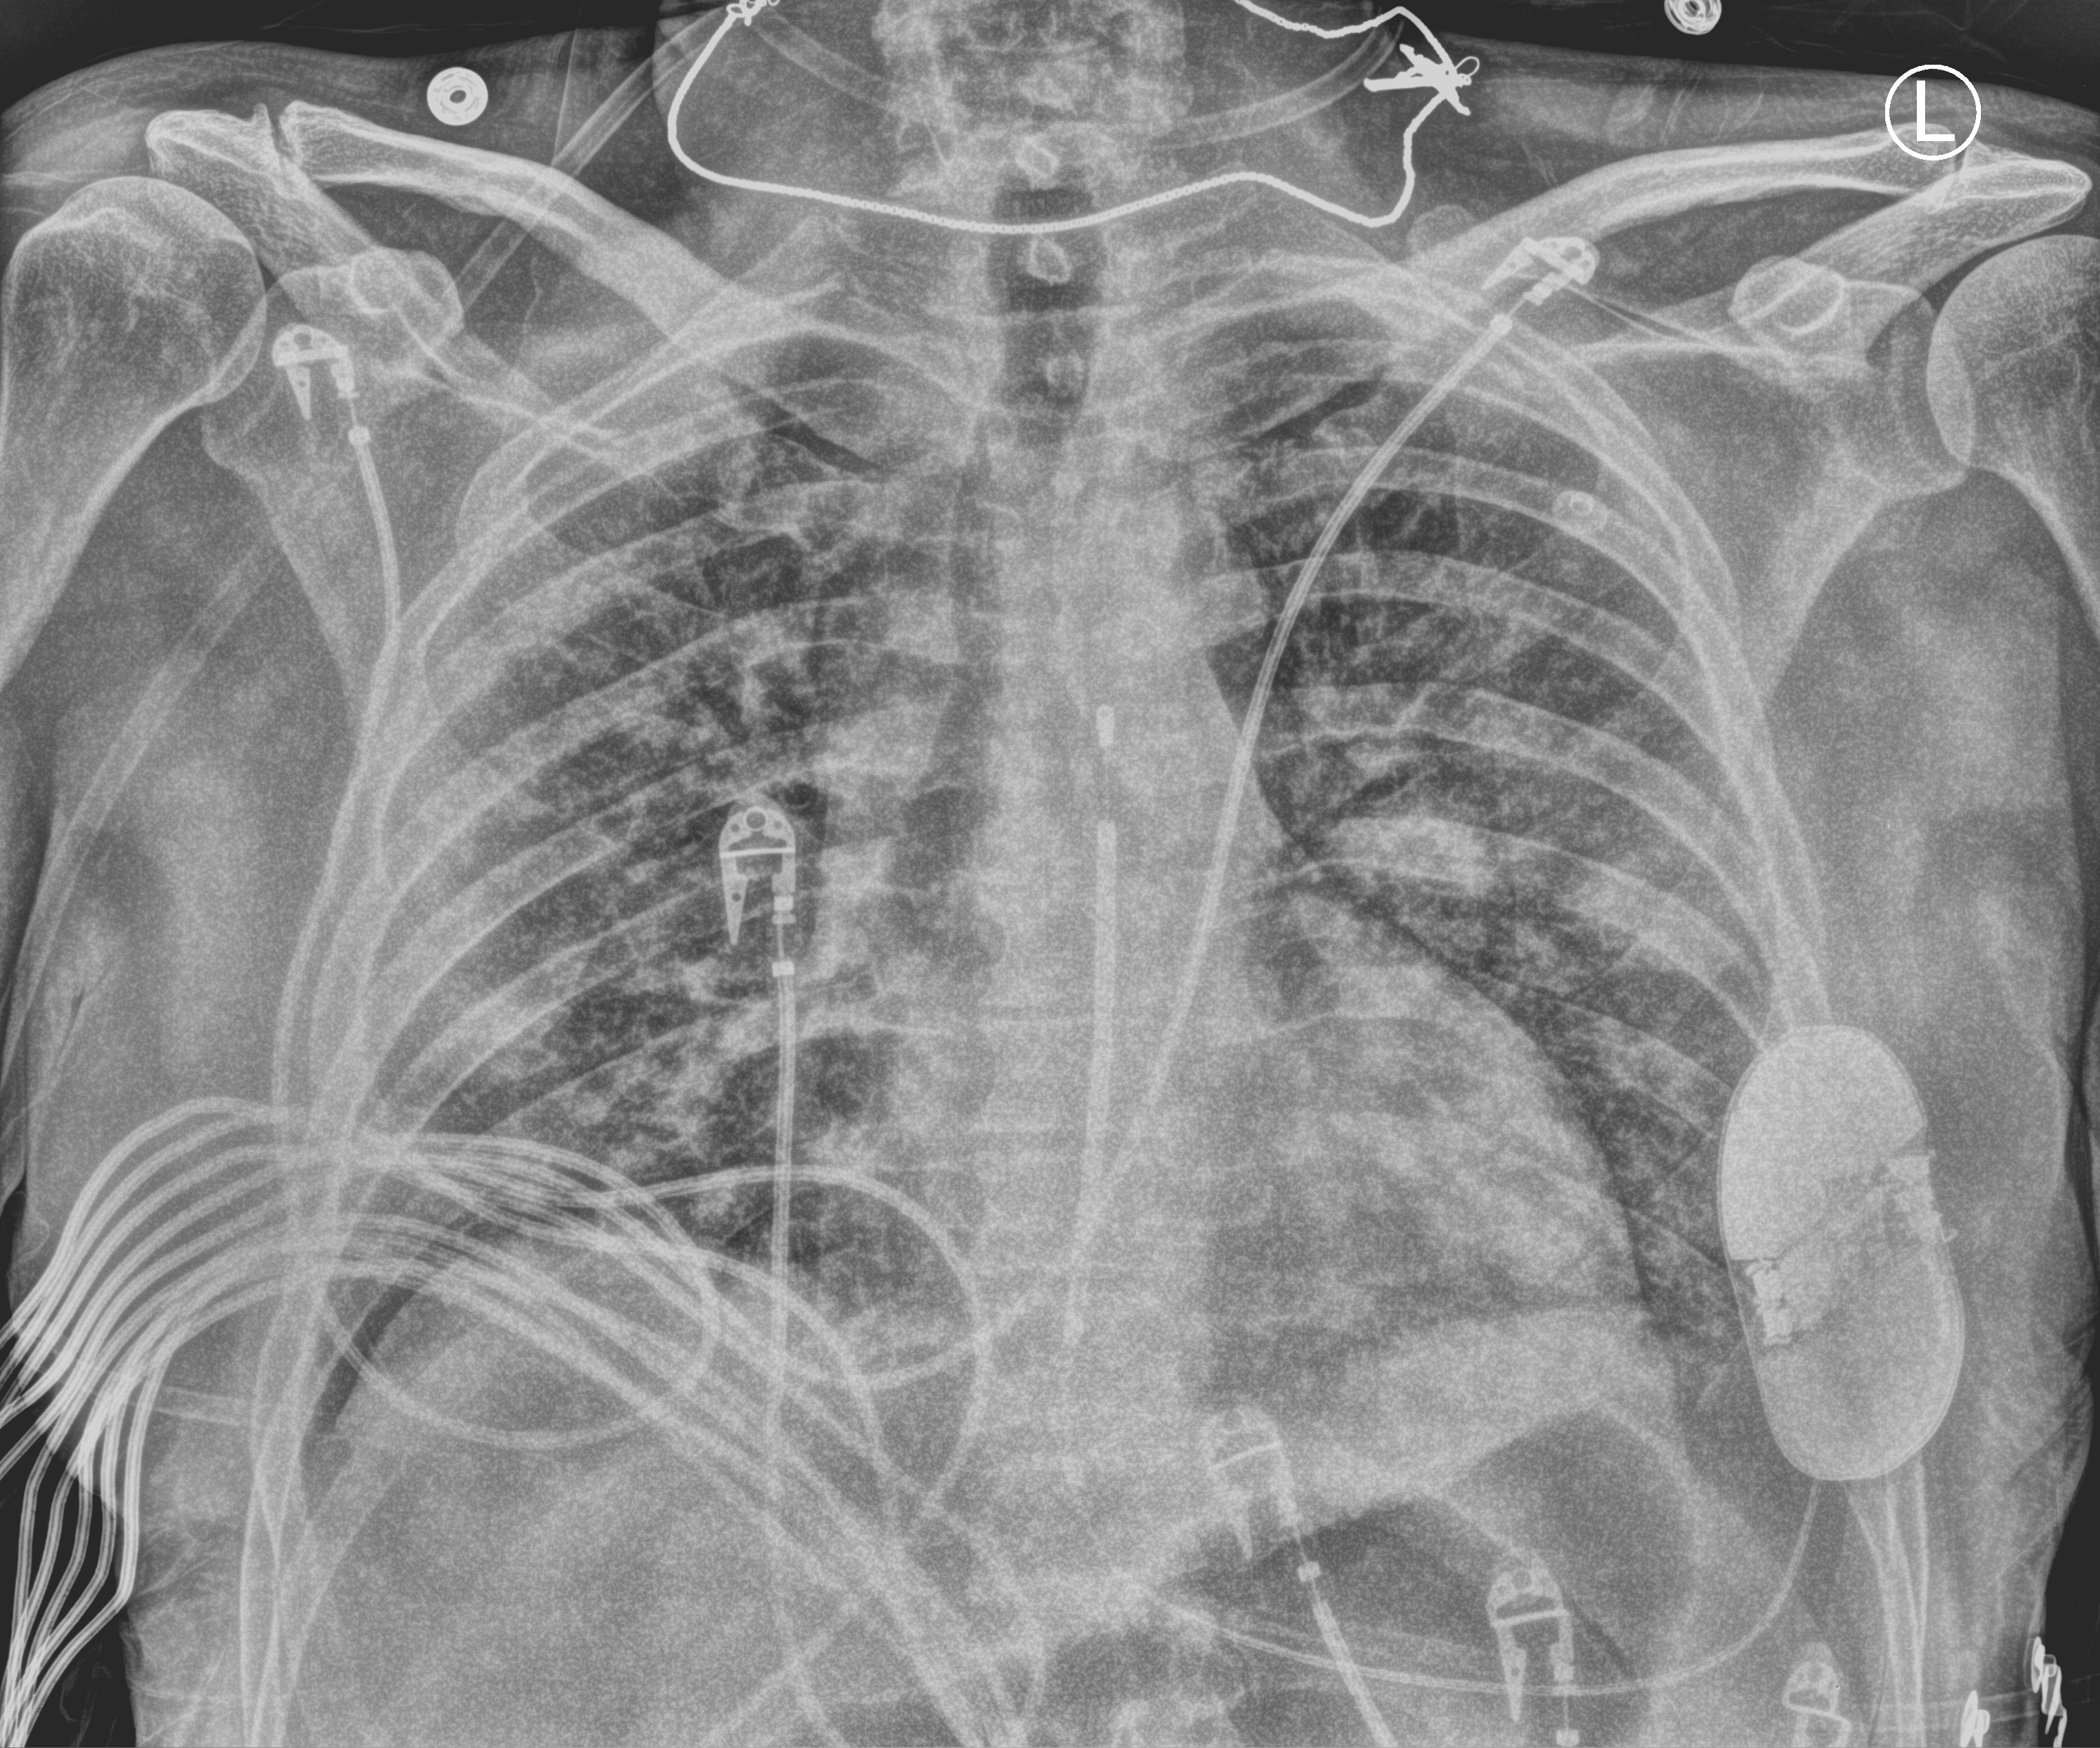
Chest X-ray (portable). Male patient hospitalised with COVID-19, age 18–59 years.
Hospital-stay facts (about this admission, not read from this image; timing relative to this image not recorded): hypertension (admission record): no.